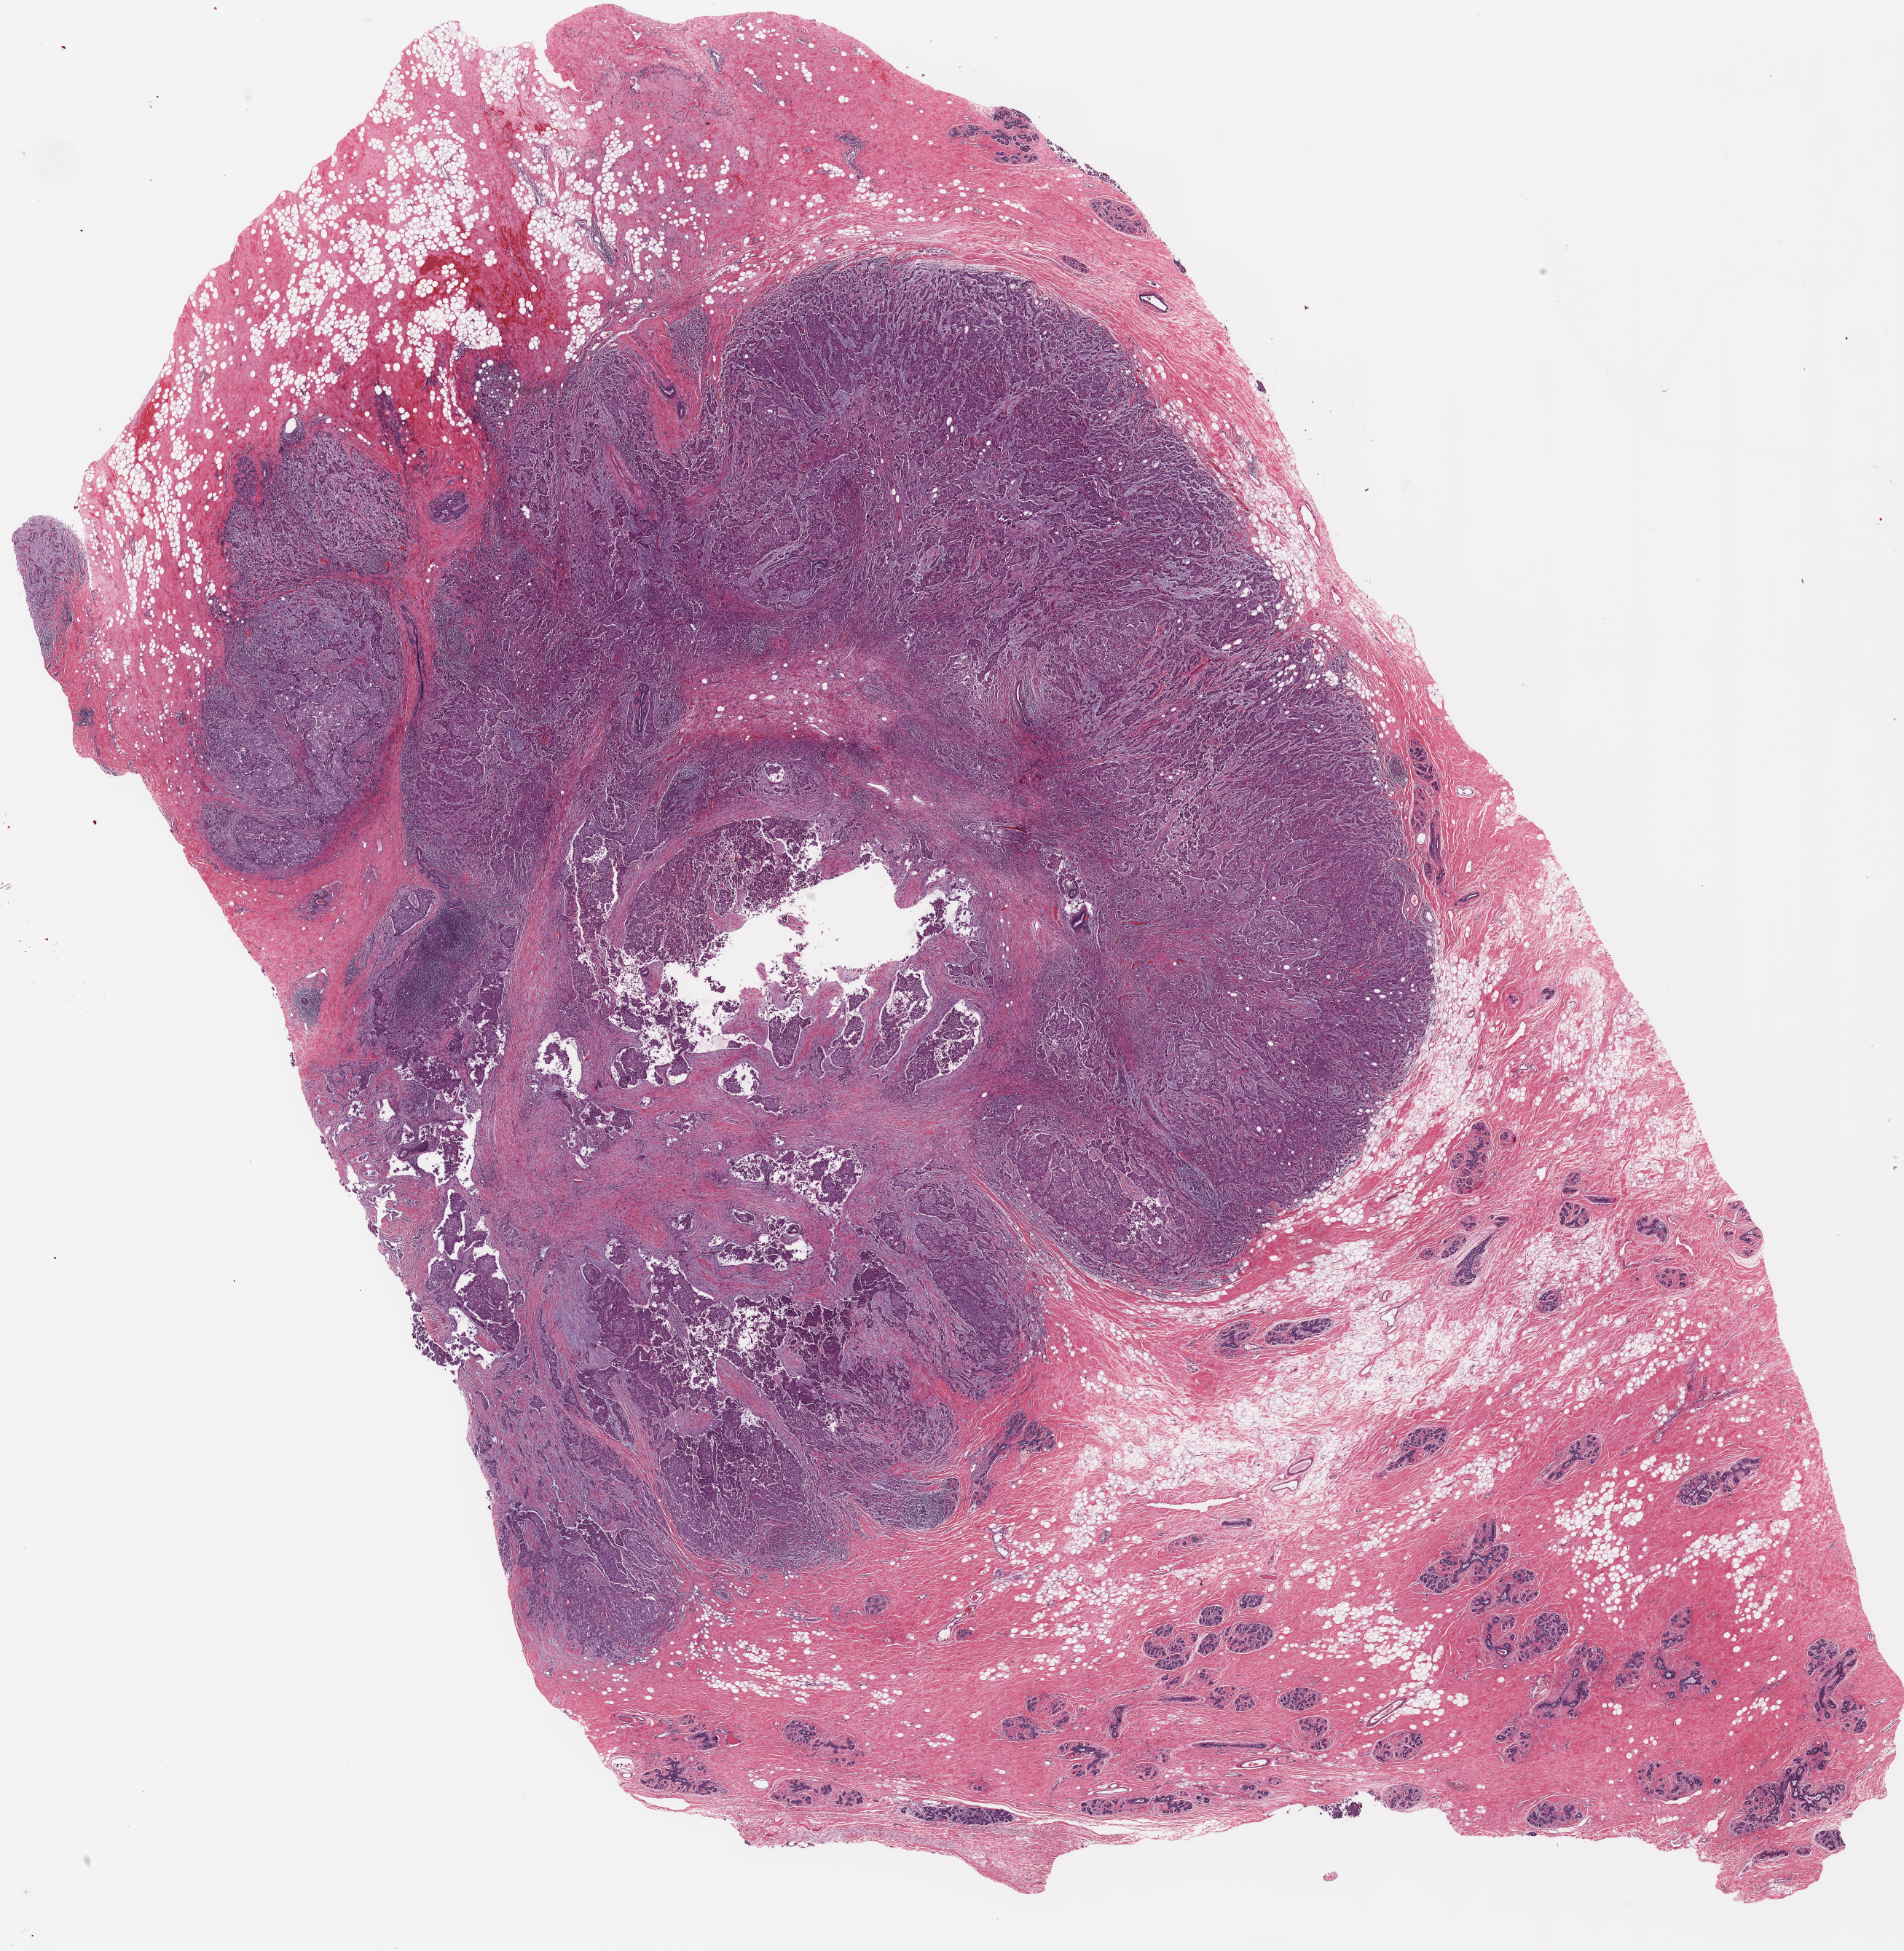
Whole-slide histology image, H&E-stained, low-resolution overview of the scanned area, about 20.9 x 21.4 mm (from a 20x scan); formalin-fixed paraffin-embedded (FFPE) diagnostic section; sample: primary tumour, breast. Patient: female, age at initial diagnosis 29 years.
* pathologic diagnosis: Infiltrating duct carcinoma, NOS
* lymph nodes positive (case pathology): 0 of 2 examined
* AJCC pathologic stage: I (6th edition)